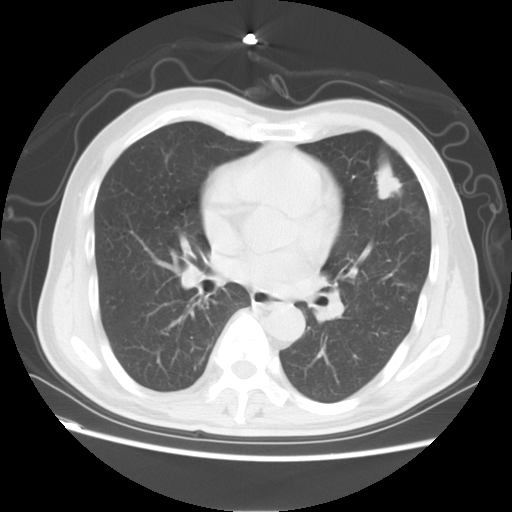
Chest CT, one axial slice. Position 32 of 64 along the scan axis. Lung window (W 1500 / L -600 HU). 5 mm slice thickness. 512 × 512 image matrix, field of view 368 × 368 mm. Patient: male, 60 years. Case-level facts recorded for this patient, not image findings: clinical TNM (as recorded): T2a N0 M0; histopathological grade: G3.
Structures marked on this image (bounding box drawn by a radiologist):
- lung tumour (recorded histology: adenocarcinoma): bounding box (x1, y1, x2, y2) in pixels: (357, 145, 415, 214)